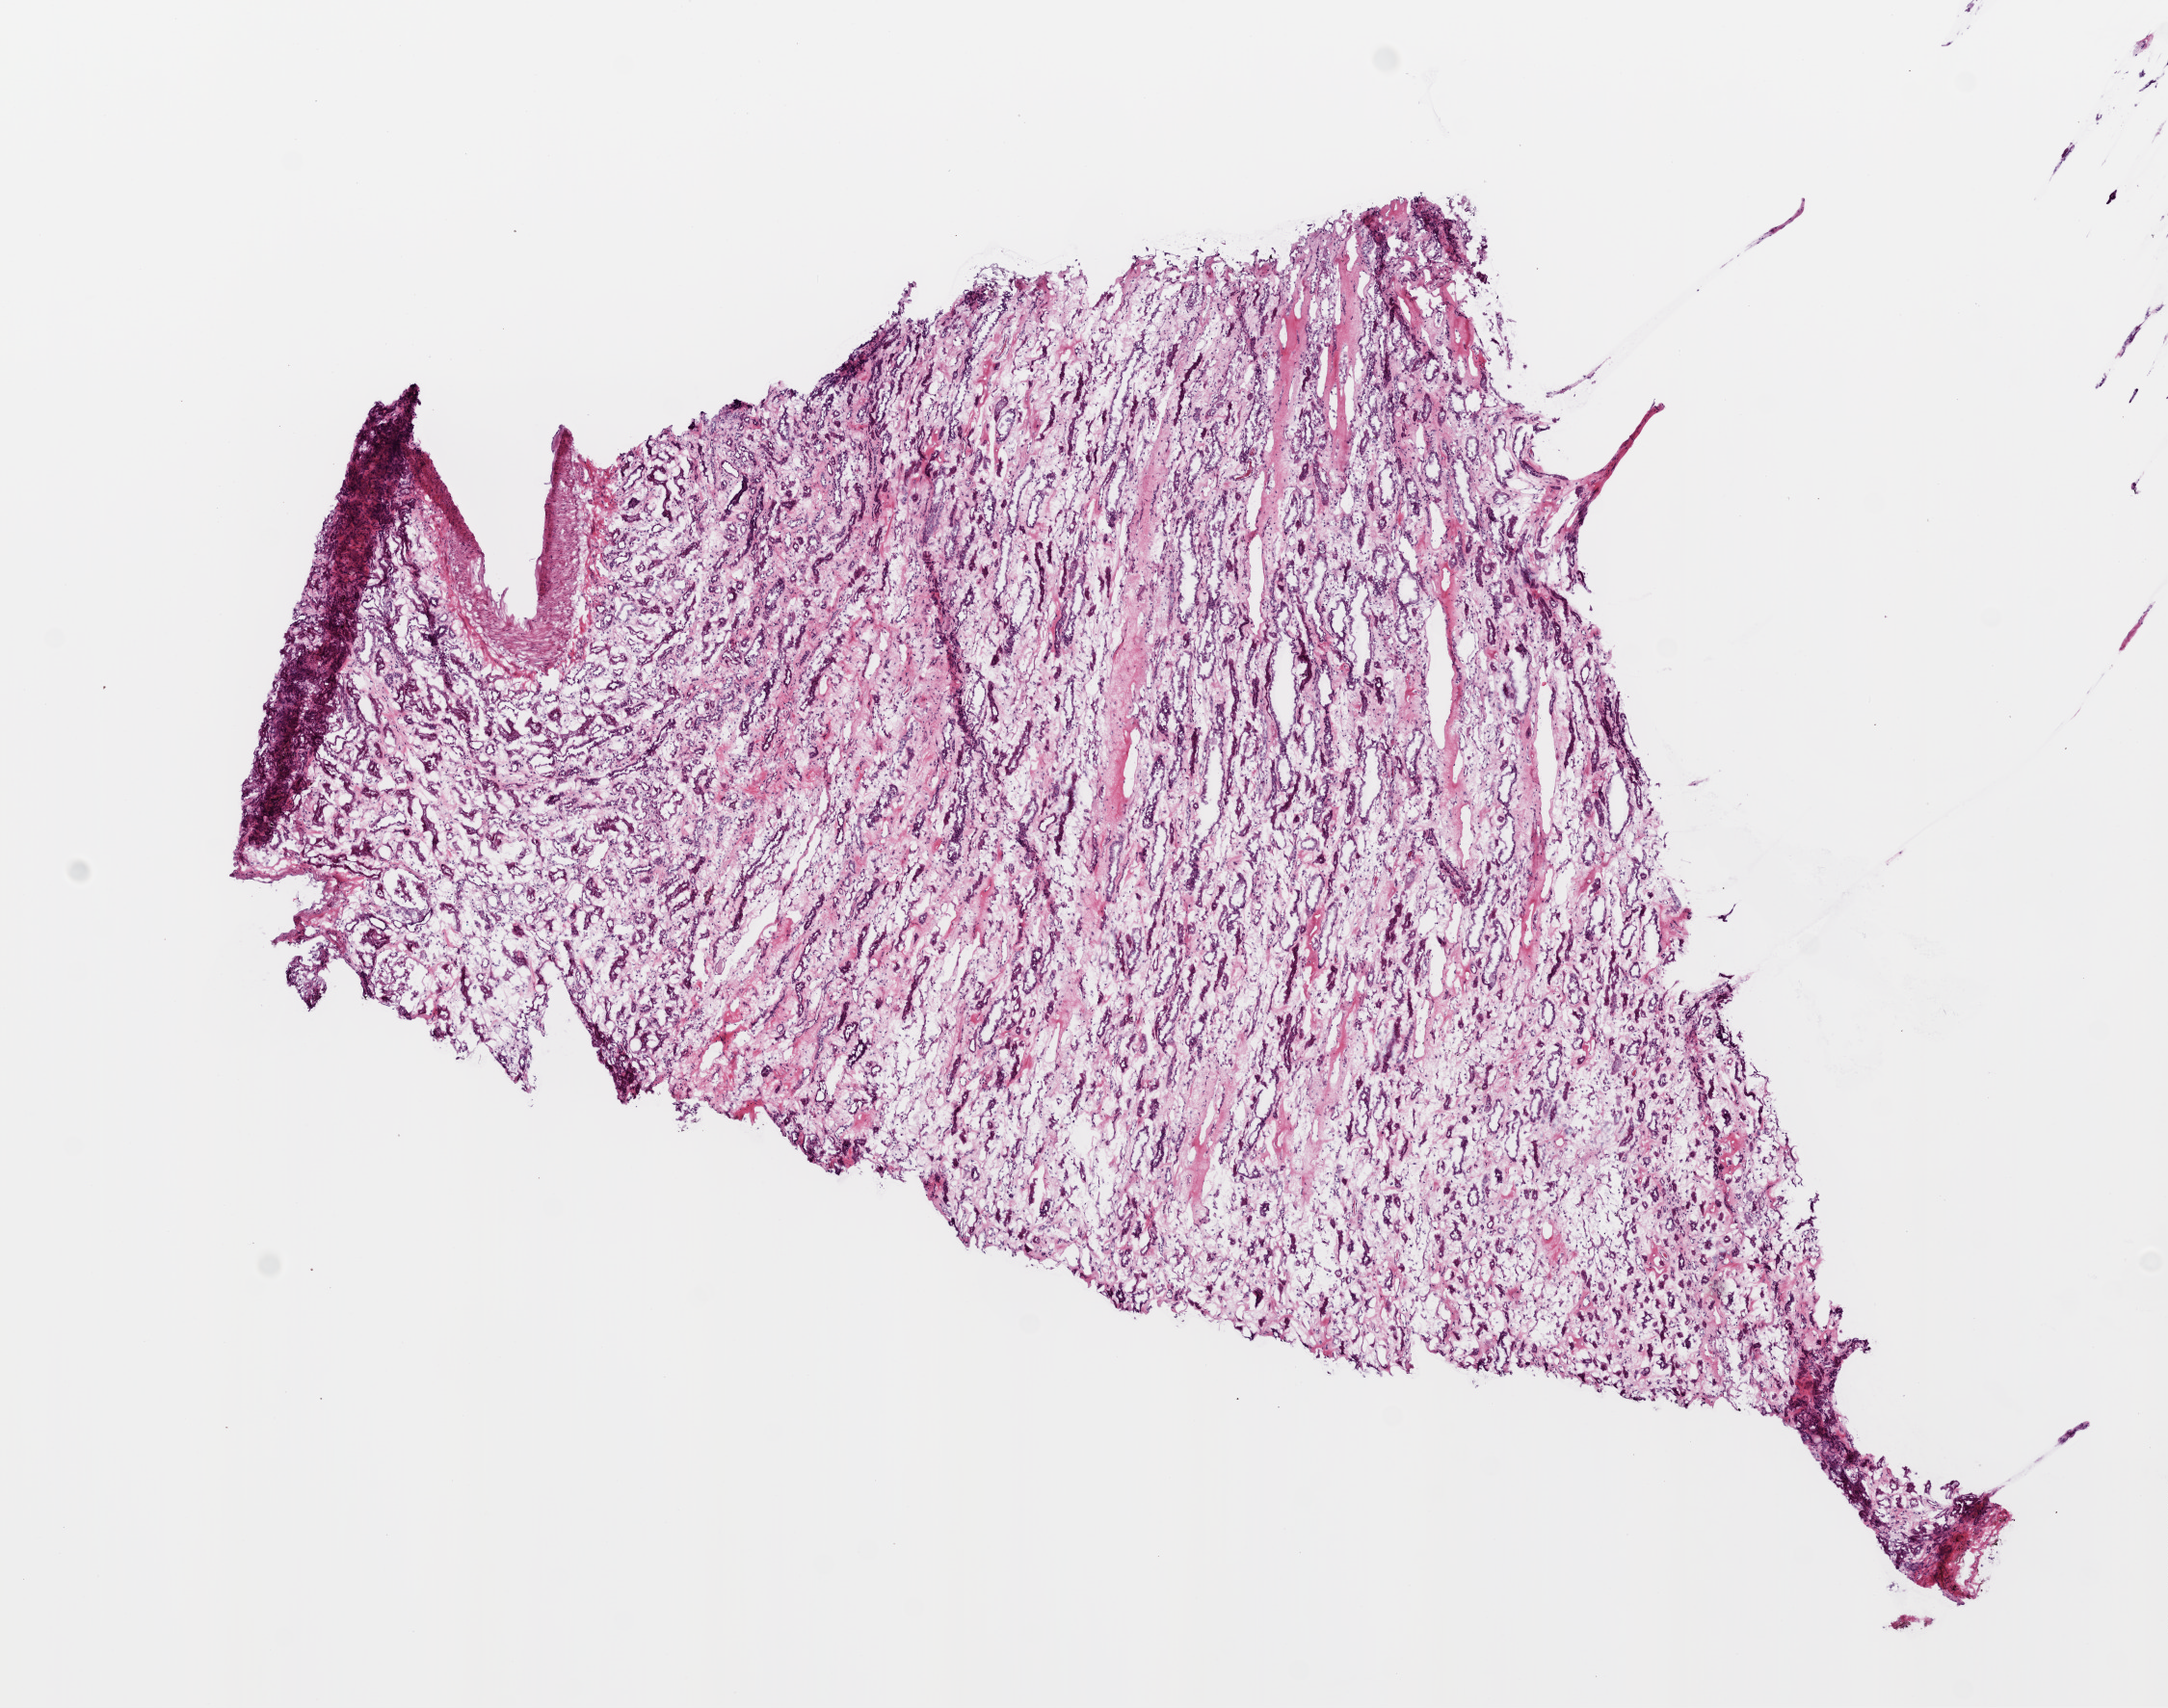
Digitized Hematoxylin and eosin (H&E) stained tissue section (whole slide) — shown as a low-resolution overview of the whole scanned area (about 9.0 x 7.1 mm), frozen section, kidney, solid tissue normal (non-tumour tissue) sample. Patient: male, age at initial diagnosis 69 years.
• this section: solid tissue normal (non-tumour) sample from the same patient
• patient diagnosis: Clear cell adenocarcinoma, NOS